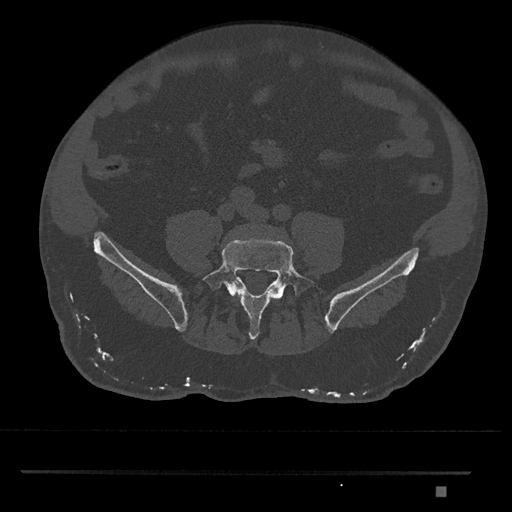
CT including the spine, one axial slice. Slice 561 of 1134 in the series (ordered by position). Bone window (W 1800 / L 400 HU). 512 × 512 image matrix. Patient: male, 65 years. From the clinical record (not read from this slice): primary cancer: prostate.
Outlined on this slice (semi-automatic segmentation, software-assisted and operator-edited):
- L4 vertebra: bounding box <235,291,238,294> (left, top, right, bottom; pixels)
- L5 vertebra: <202,239,317,340>